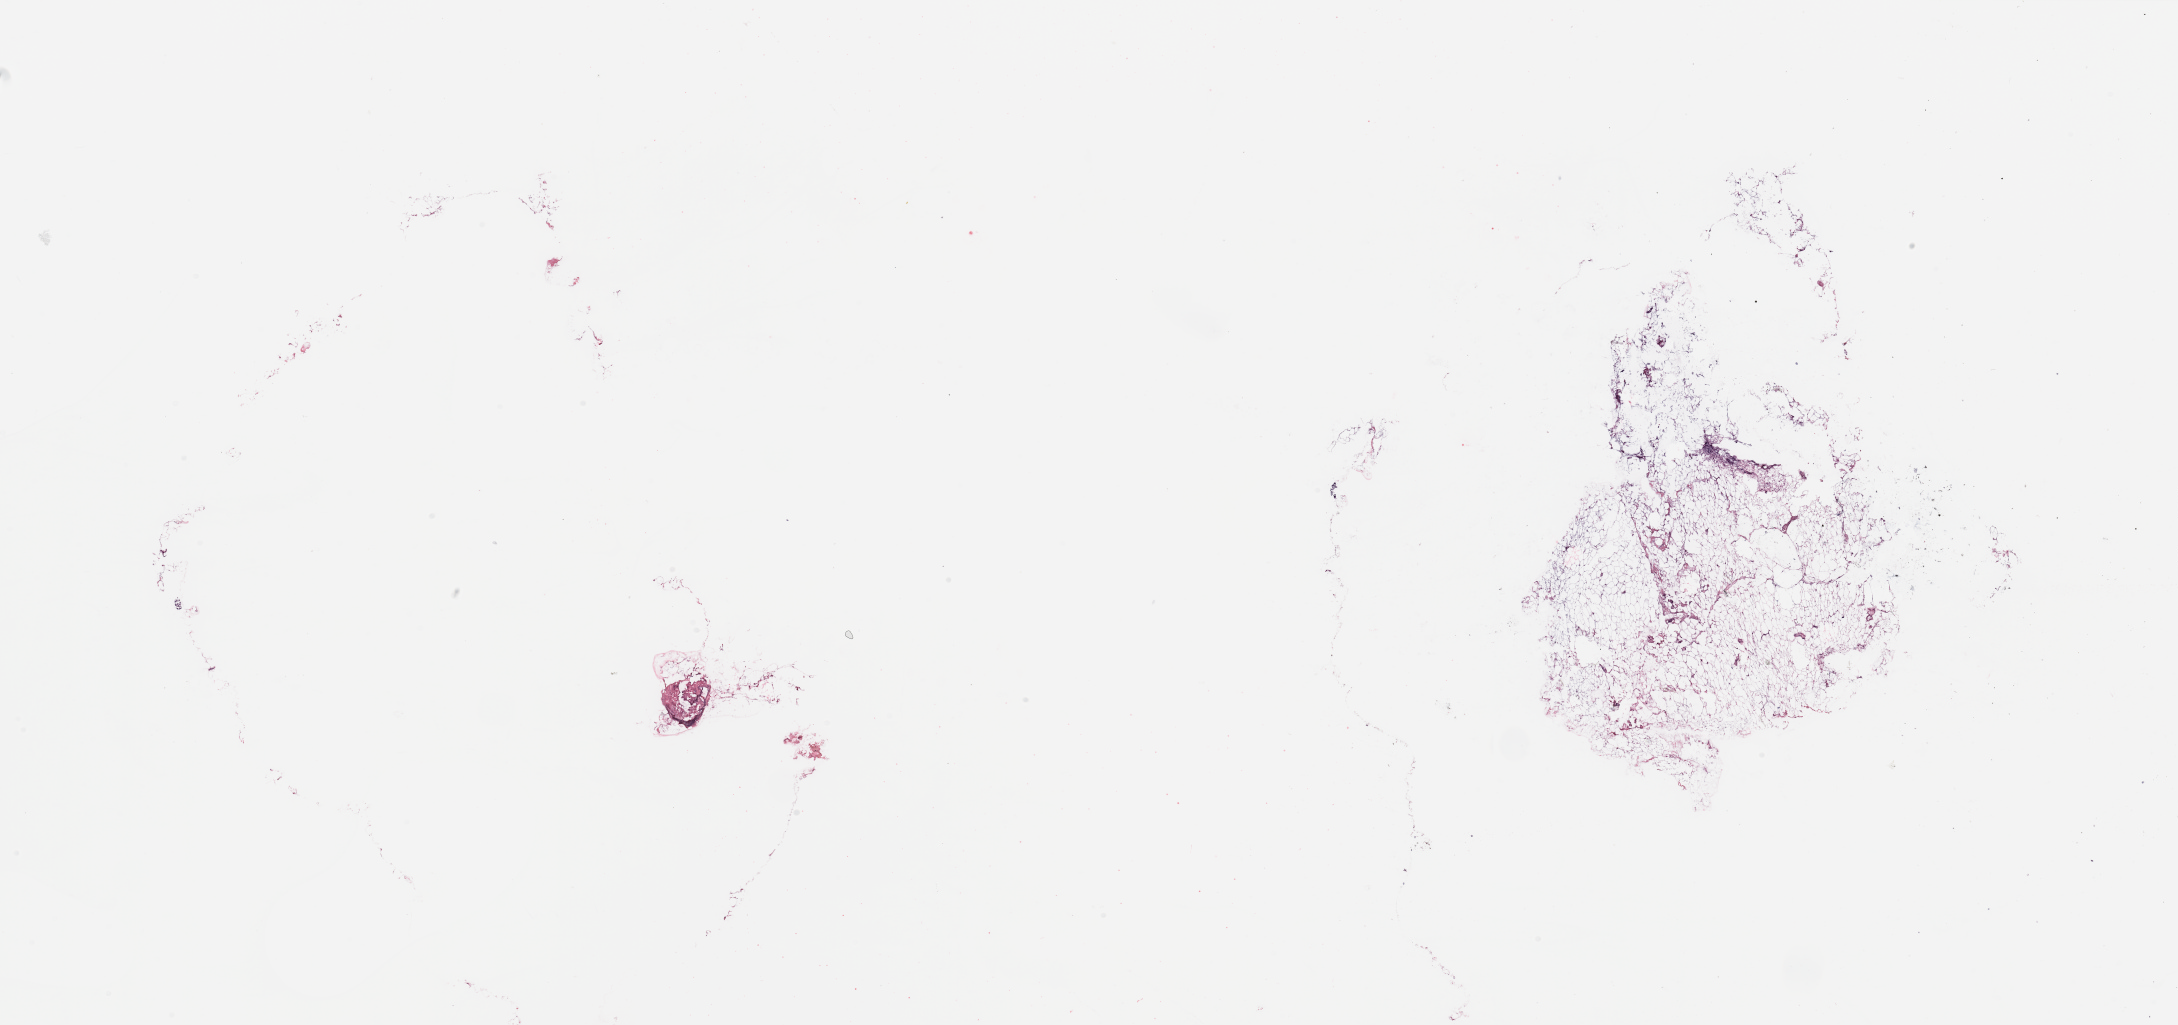
Whole-slide histology image, H&E-stained — whole scanned area (about 34.5 x 16.2 mm, acquisition: 20x scan) shown as a low-resolution overview. Breast, tumour tissue. Female, 70 y/o.
Diagnosis: Infiltrating duct carcinoma, NOS. AJCC pathologic stage: IIIC.